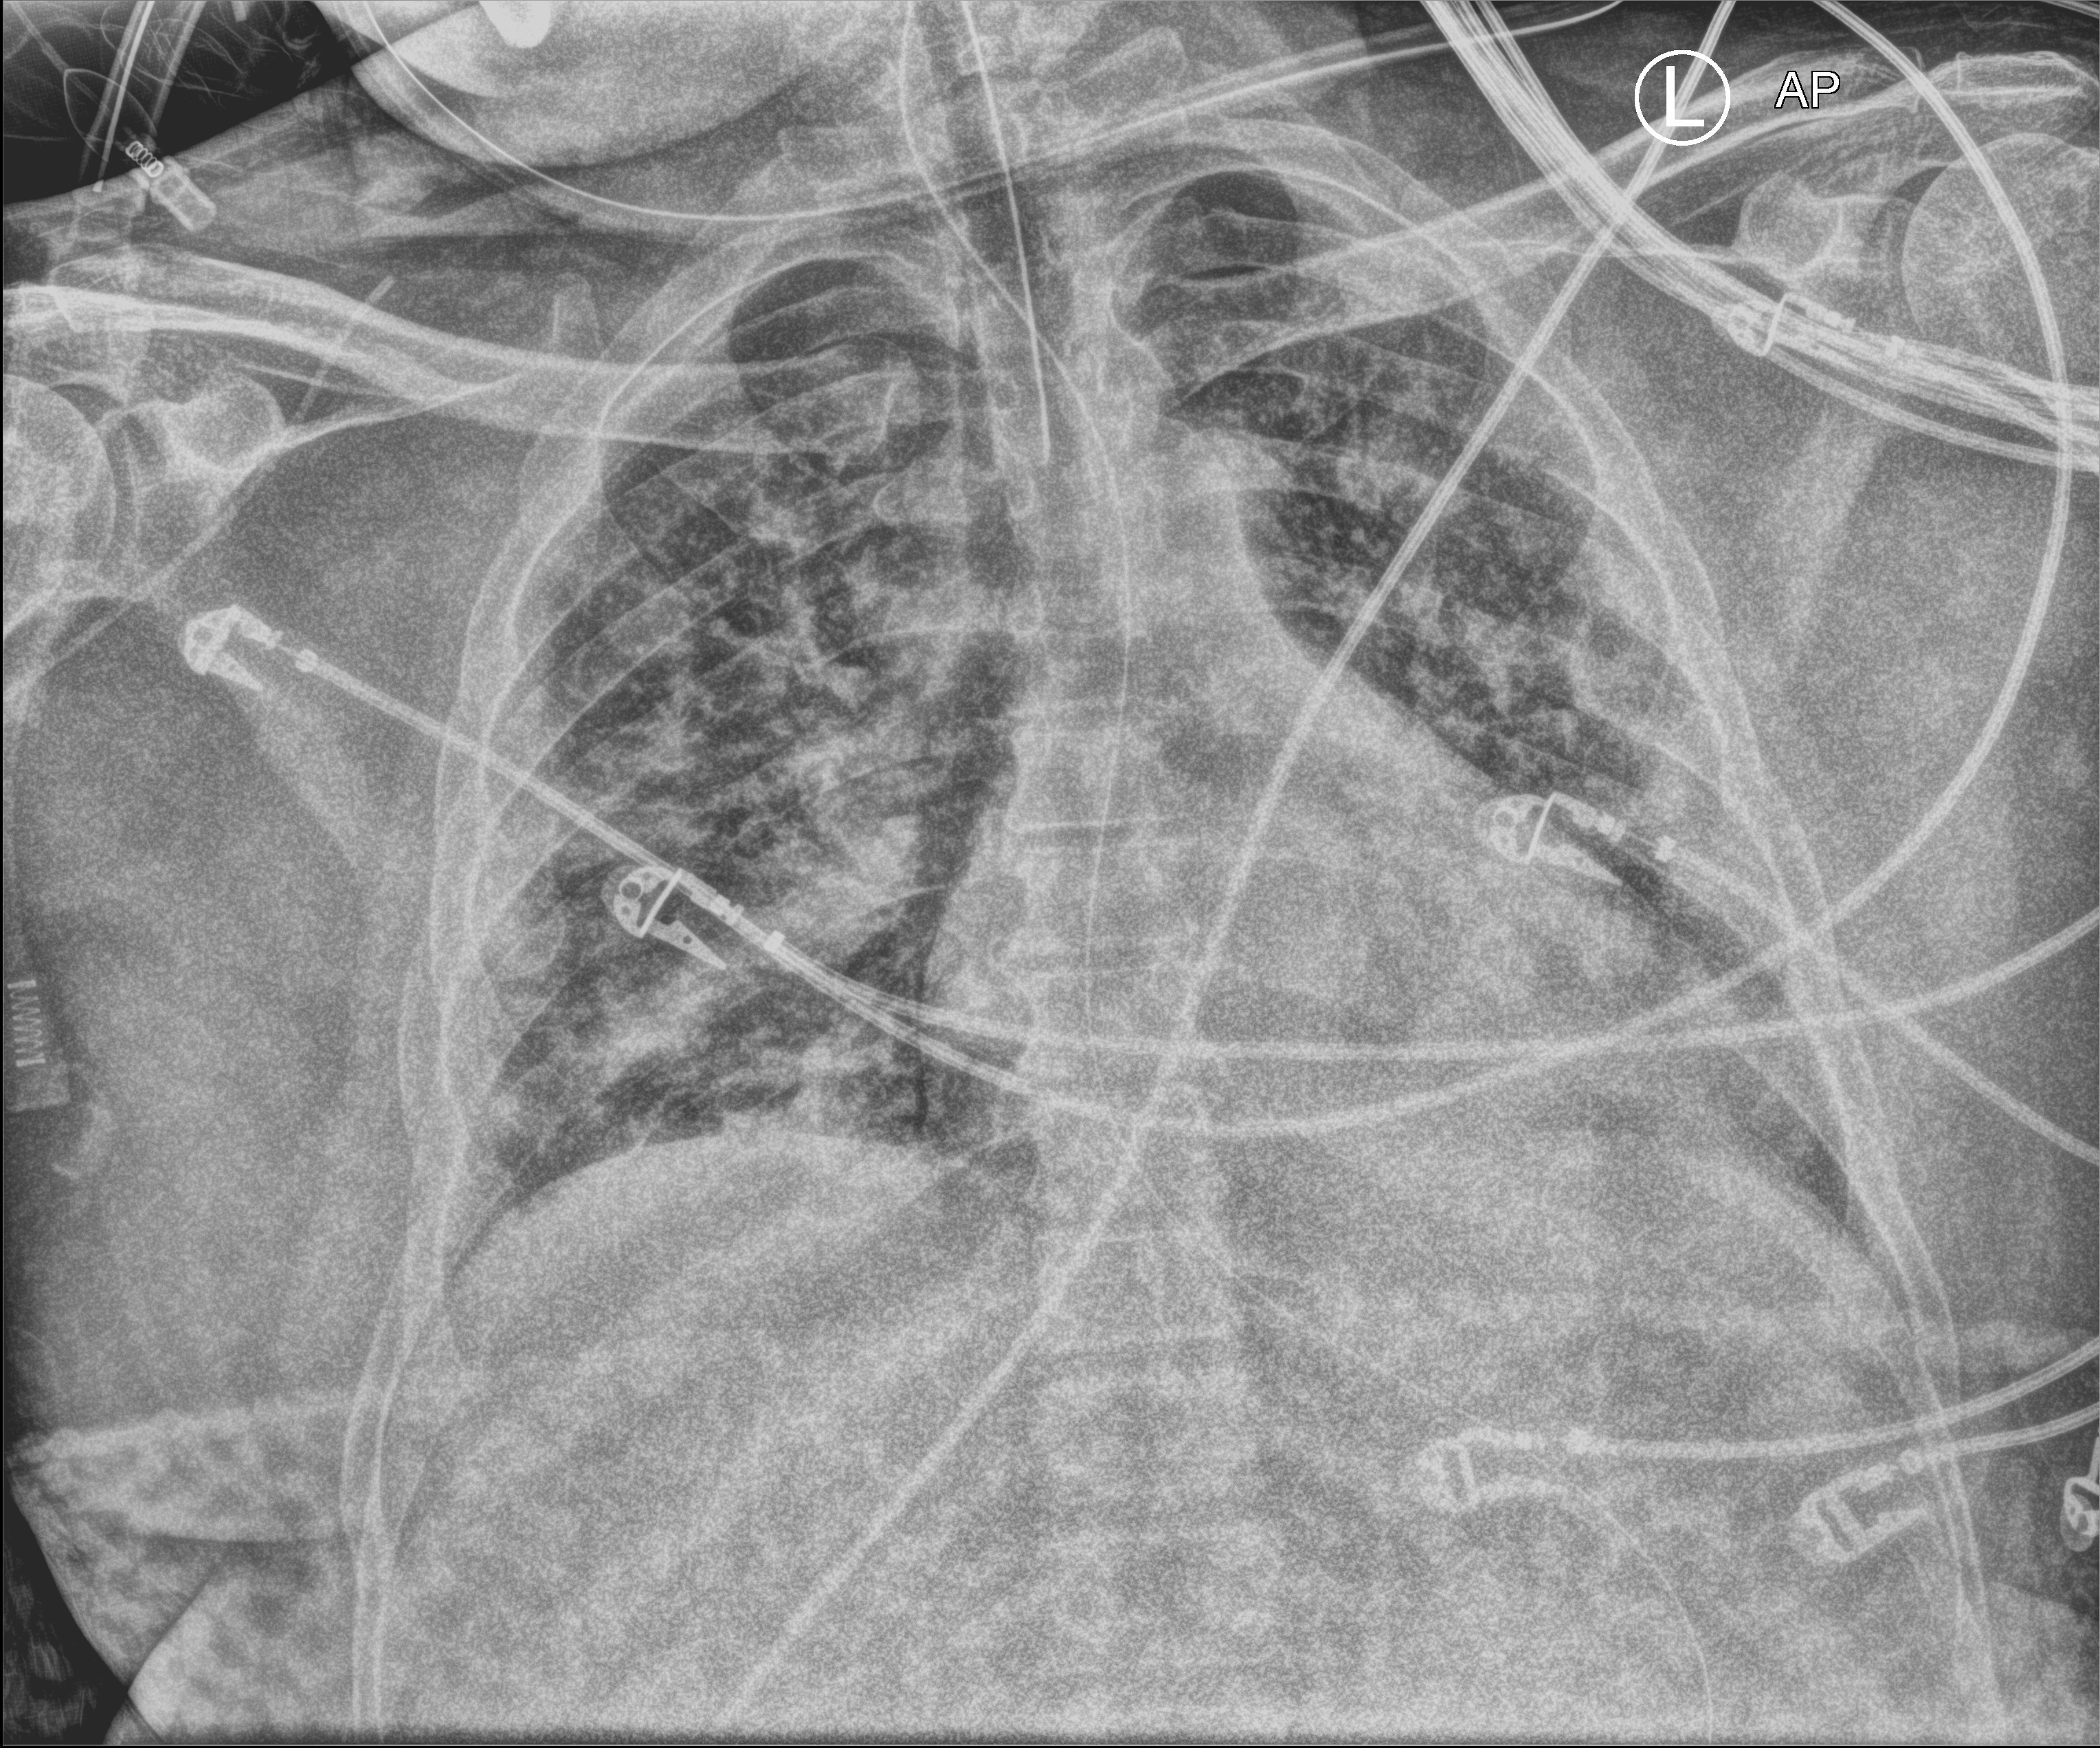
Portable chest radiograph, anteroposterior (AP) projection. Patient hospitalised with COVID-19; male, aged 18–59 years.
Admission-level facts for this patient (not findings on this image; timing relative to this image not recorded): diabetes (admission record): no; mechanically ventilated during this hospital stay: yes; length of hospital stay: 15 days.